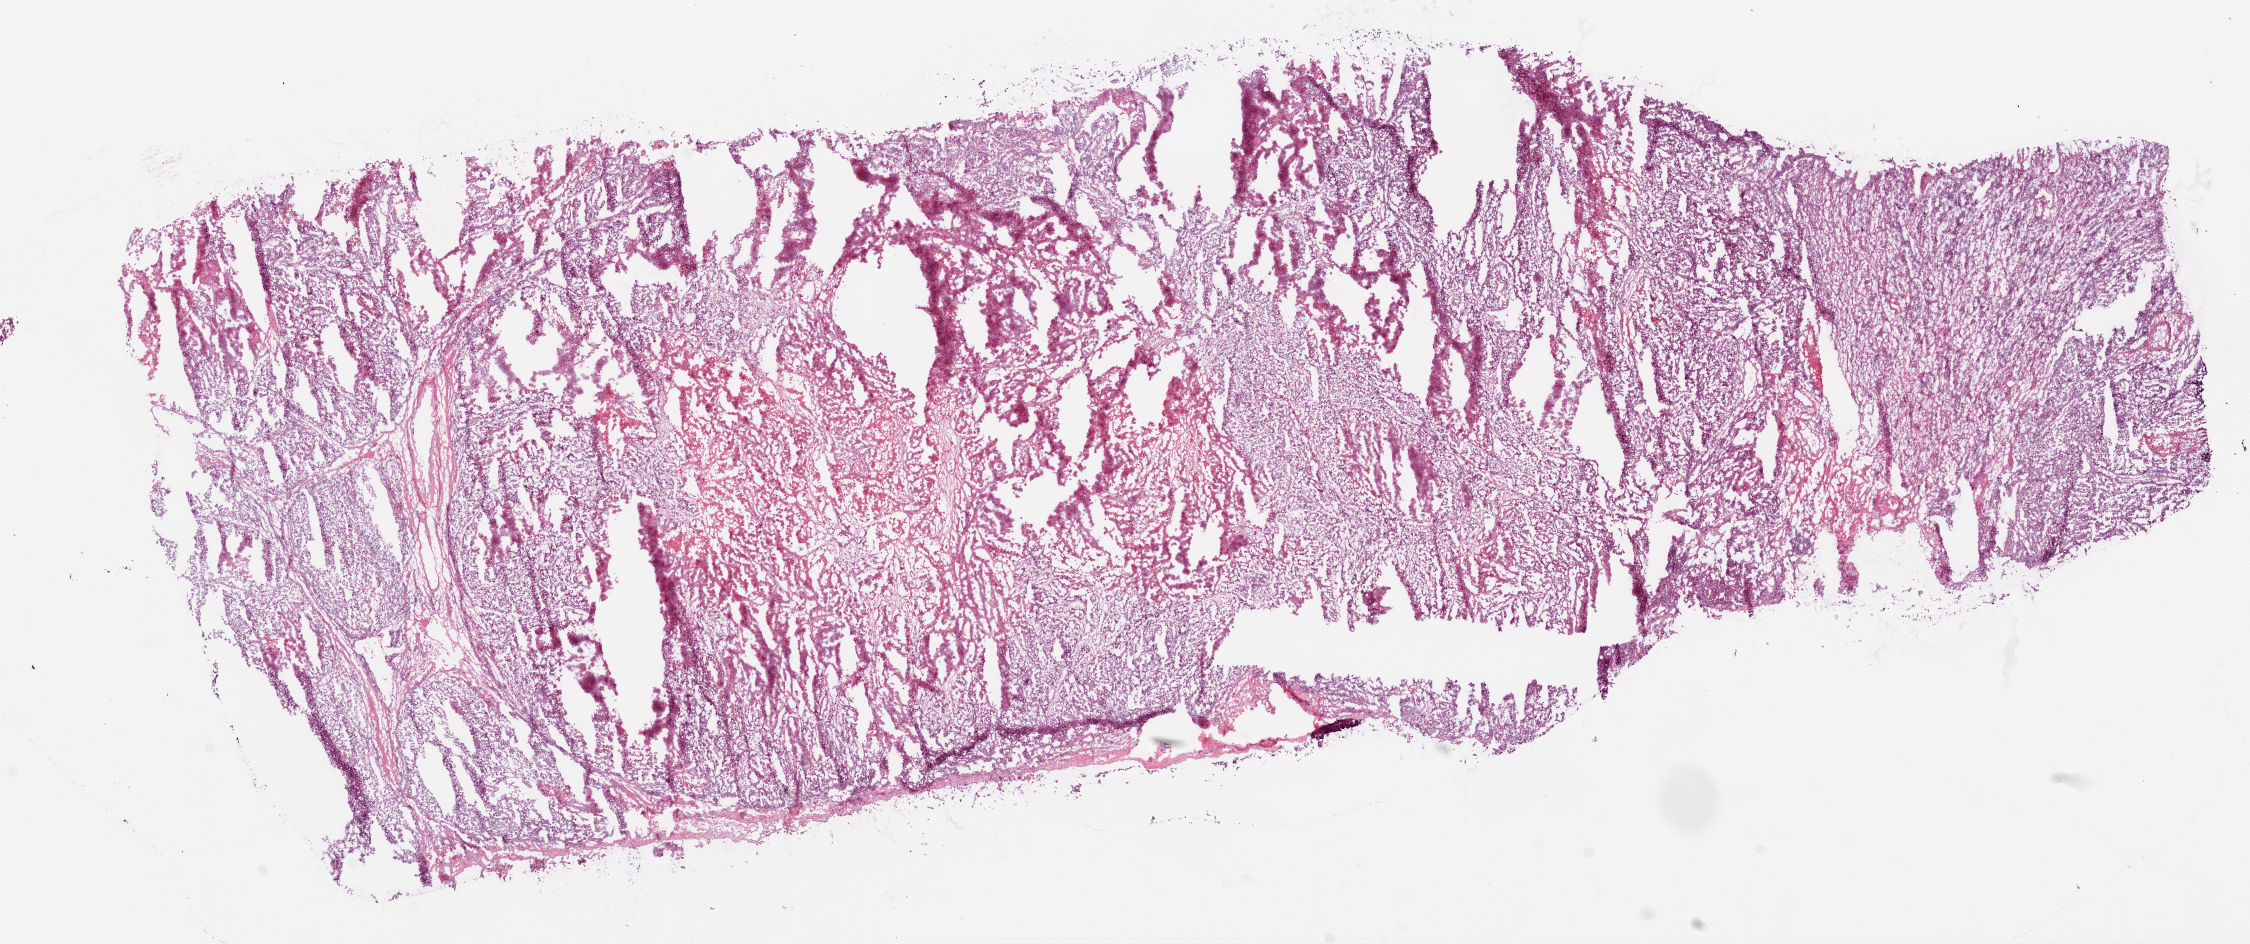
Whole-slide histology image, H&E-stained, a low-resolution overview of the entire scanned area, about 18.1 x 7.6 mm (acquisition: 20x scan); frozen section; primary tumour sample from the kidney. Male, age 69 years at initial diagnosis. Histologic grade: G4 (undifferentiated). Slide review estimates, as recorded: tumour cells 70%, tumour nuclei 80%, normal cells 0%, stromal cells 10%, necrosis 20%.
TNM: T3b N1 M0. AJCC pathologic stage: III. Lymph nodes positive (case pathology): 1 of 1 examined. Histologic diagnosis: Clear cell adenocarcinoma, NOS.